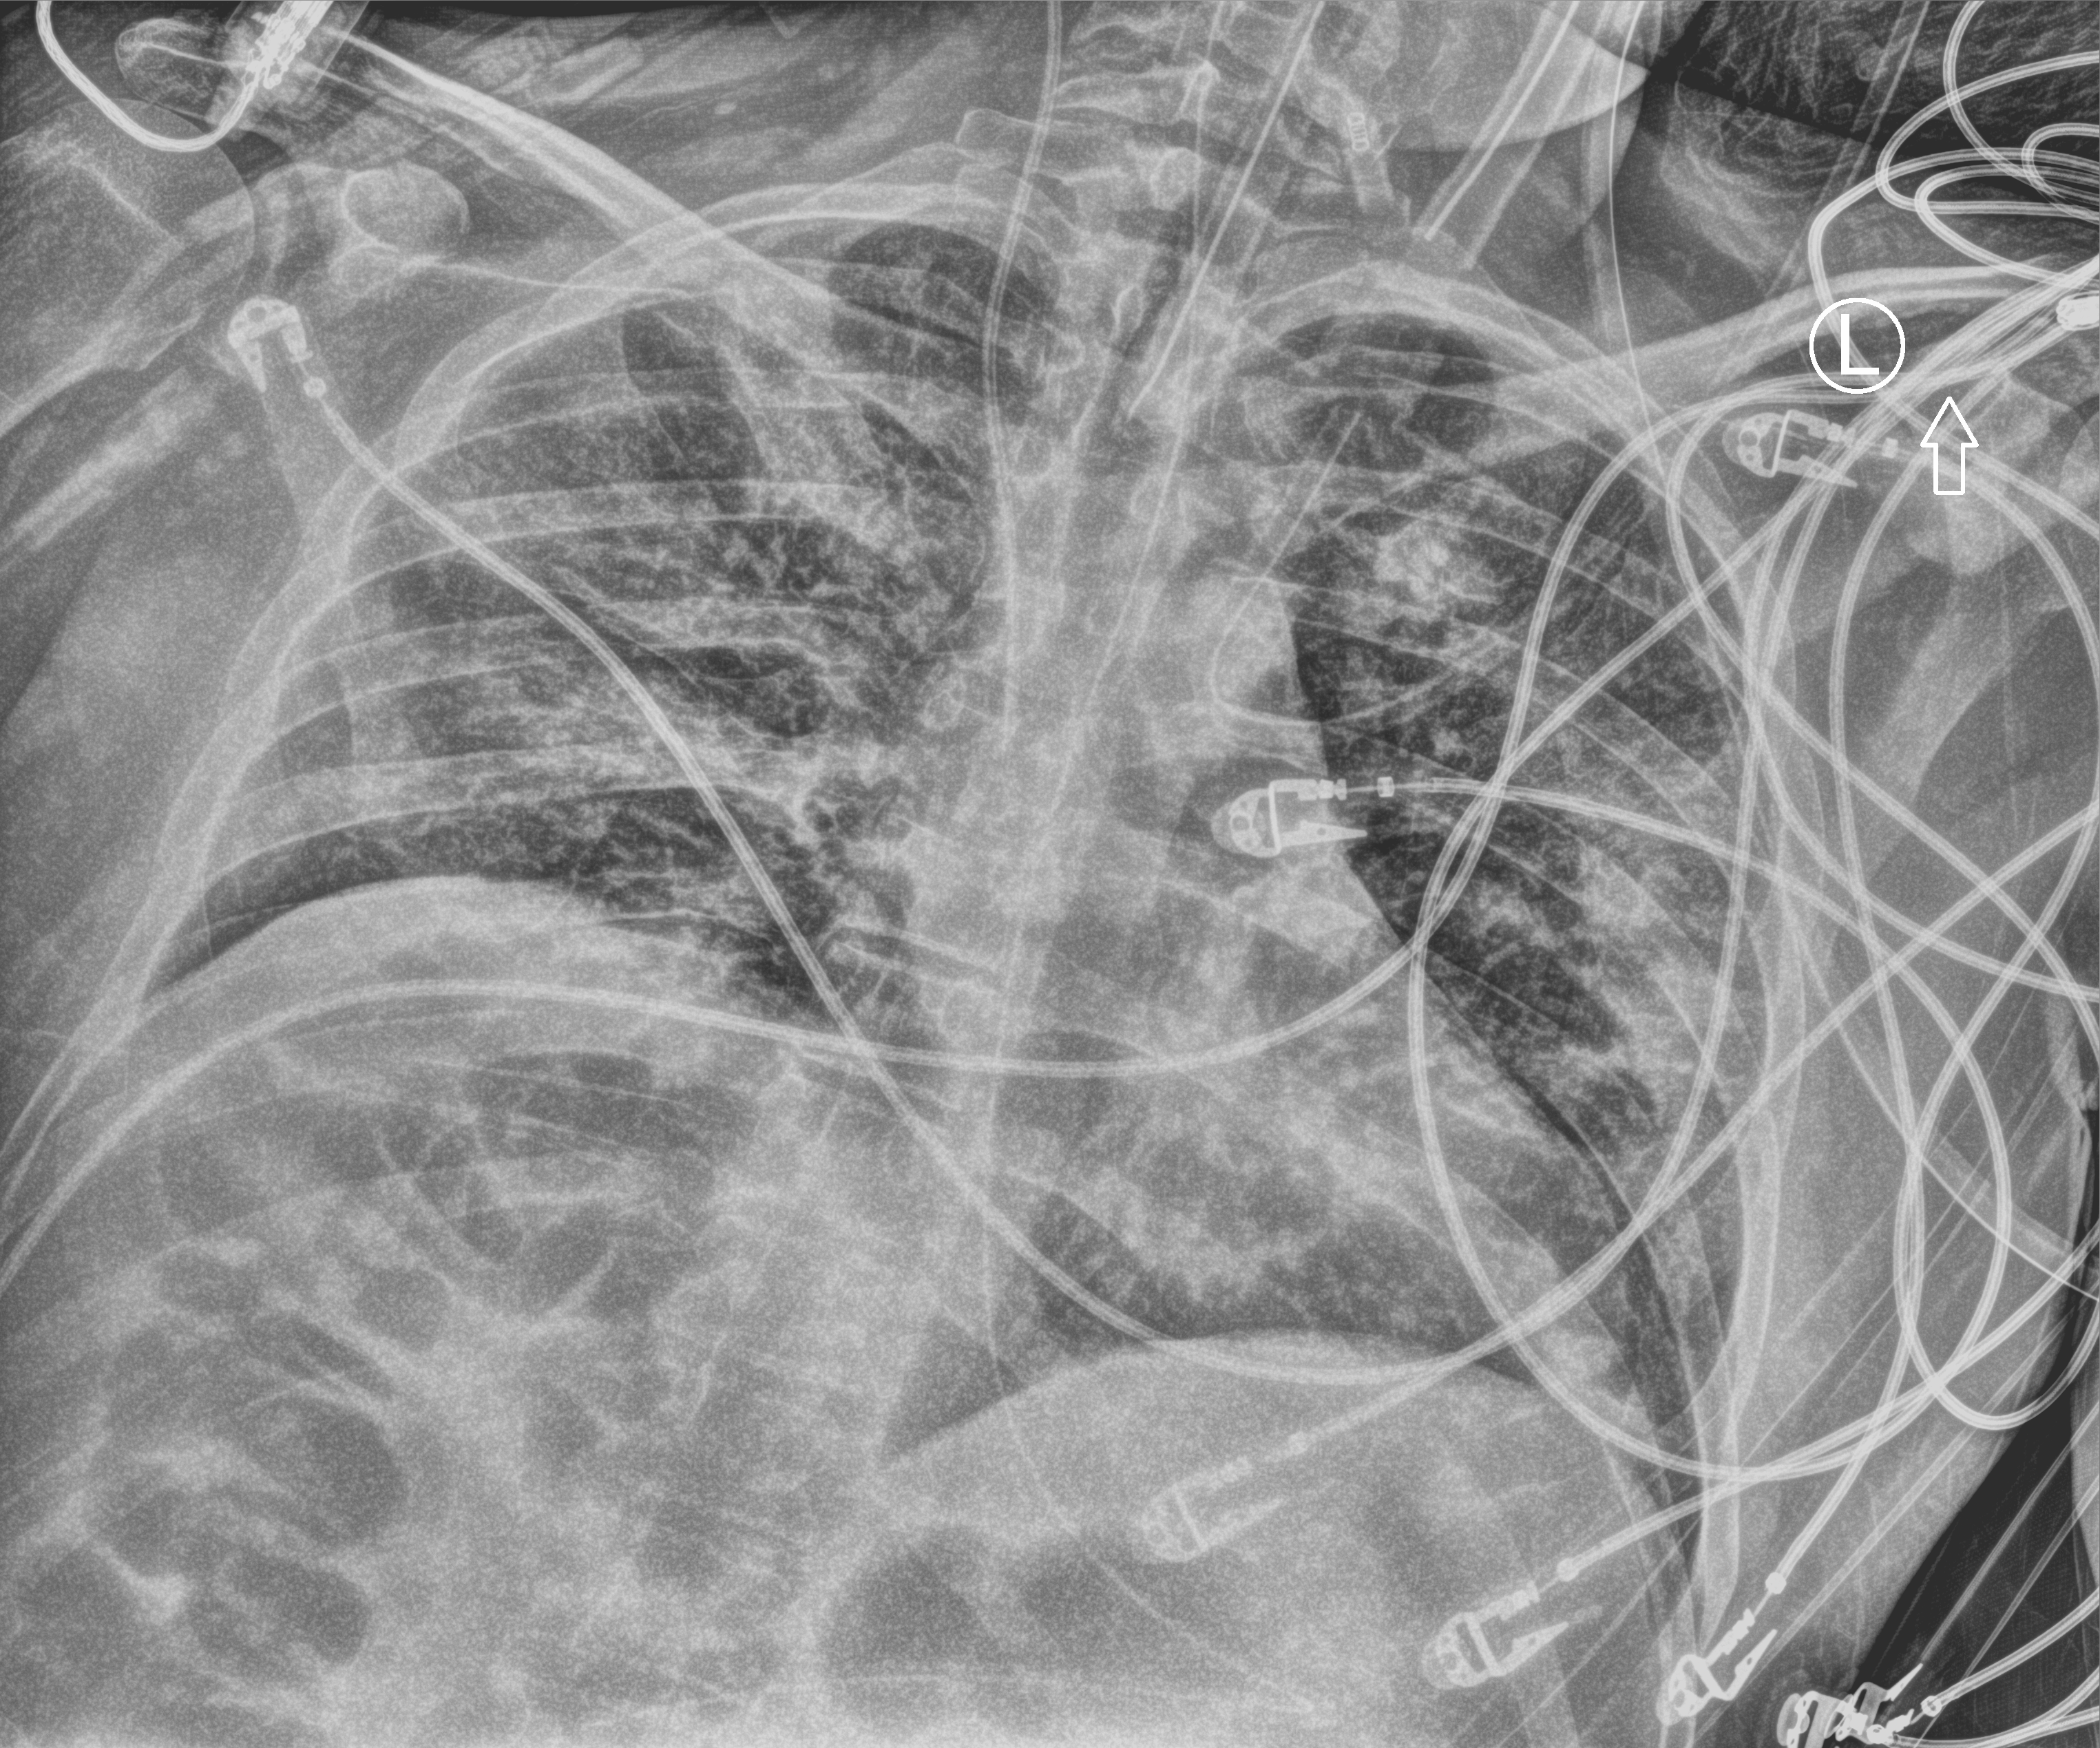
Portable chest radiograph; anteroposterior (AP) projection. Patient hospitalised with COVID-19; male, aged 18–59 years.
Hospital-stay facts (about this admission, not read from this image; timing relative to this image not recorded): length of hospital stay: 48 days.